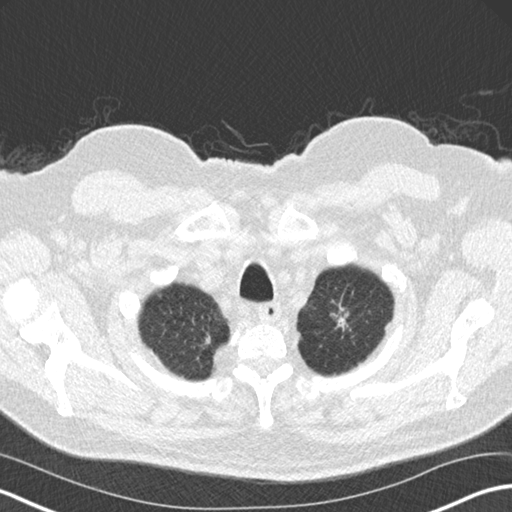
Low-dose screening chest CT, one axial slice. Slice 152 of 175 in the series (ordered by position). 120 kVp. Lung window (W 1500 / L -600 HU). 2 mm slice thickness. 512 × 512 image matrix, field of view 351 × 351 mm.
Annotated regions visible in this slice (expert manual segmentation):
- lesion 1 (tumor, upper lobe of left lung): bounding box <333,310,351,337> (left, top, right, bottom; pixels)